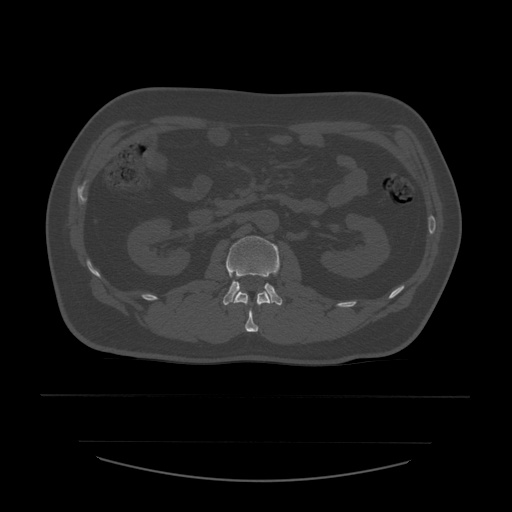
CT including the spine, one axial slice. Slice 211 of 532 in the series (ordered by position). Reconstruction kernel STANDARD. Bone window (W 1800 / L 400 HU). 1.25 mm slice thickness. 512 × 512 image matrix. Patient age 44 years. From the clinical record (not read from this slice): primary cancer: soft tissue sarcoma.
Structures marked on this image (semi-automatically segmented with operator editing):
- L1 vertebra: box from (x=233, y=291) to (x=273, y=332) px
- L2 vertebra: (x=223, y=236)–(x=283, y=306)